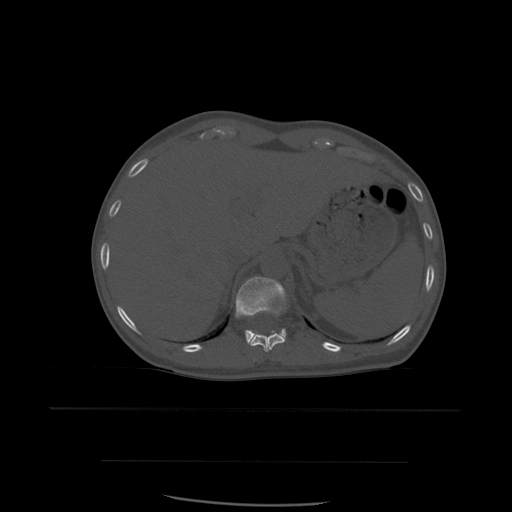
CT including the spine, one axial slice. Position 287 of 574 along the scan axis. Bone window (W 1800 / L 400 HU). 1.25 mm slice thickness. 512 × 512 image matrix, field of view 392 × 392 mm. Patient age 48 years. From the clinical record (not read from this slice): primary cancer: lung; vertebrae with lytic lesions (as recorded): T11.
Annotated regions visible in this slice (semi-automatically segmented with operator editing):
- T11 vertebra: bounding box <249,311,286,352> (left, top, right, bottom; pixels)
- T12 vertebra: <236,277,287,344>